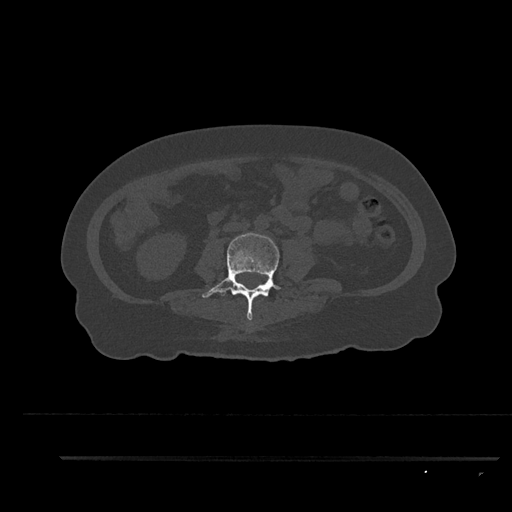
CT including the spine, one axial slice; position 84 of 797 along the scan axis; reconstruction kernel Br40s/3; bone window (W 1800 / L 400 HU); 0.5 mm slice thickness; 512 × 512 image matrix, field of view 408 × 408 mm. Patient: female, 44 years. From the clinical record (not read from this slice): primary cancer: renal.
Annotated regions visible in this slice (semi-automatically segmented with operator editing):
- L3 vertebra: bounding box (x1, y1, x2, y2) in pixels: (202, 232, 281, 320)